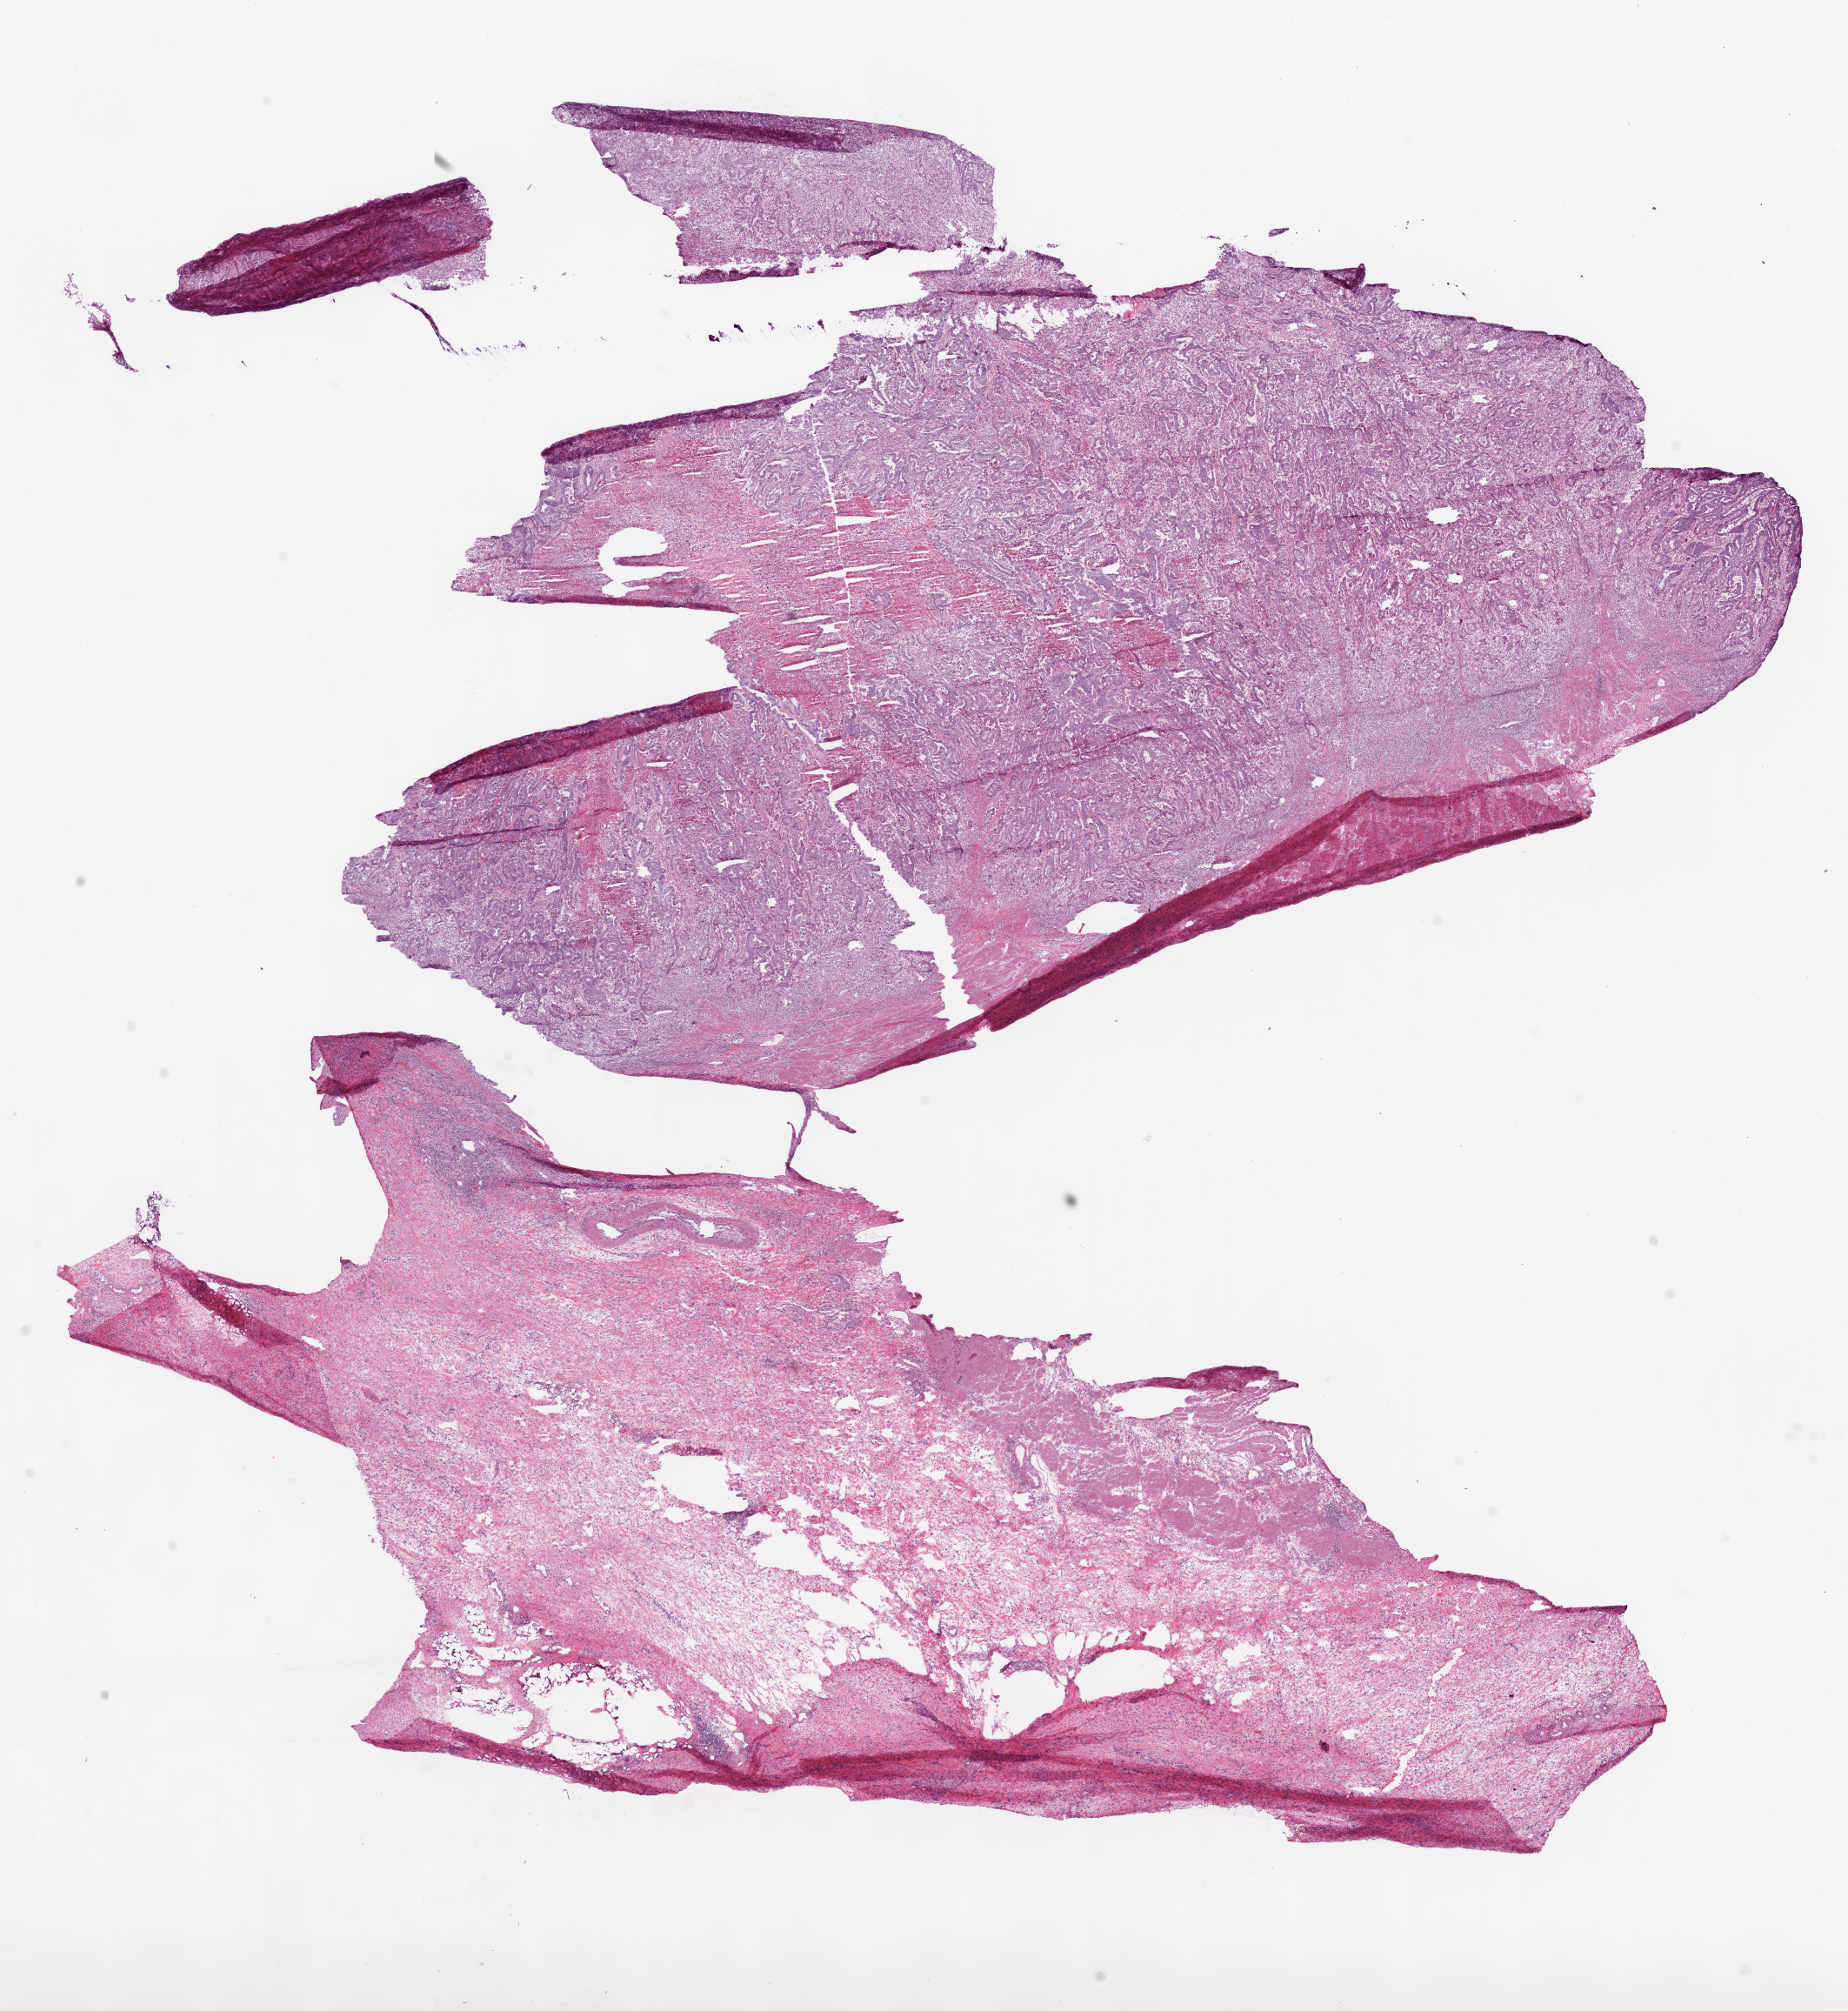
Whole-slide histology image, H&E — whole scanned area (about 17.1 x 18.6 mm, acquisition: 20x scan) shown as a low-resolution overview, frozen section, sample: primary tumour, stomach. Patient: female, age at initial diagnosis 66 years. Histologic grade: G1 (well differentiated). Composition of this section per pathologist review: tumour cells 40%, tumour nuclei 75%, normal cells 40%, stromal cells 10%, necrosis 10%.
• pathologic diagnosis: Adenocarcinoma, NOS (cardia, NOS)